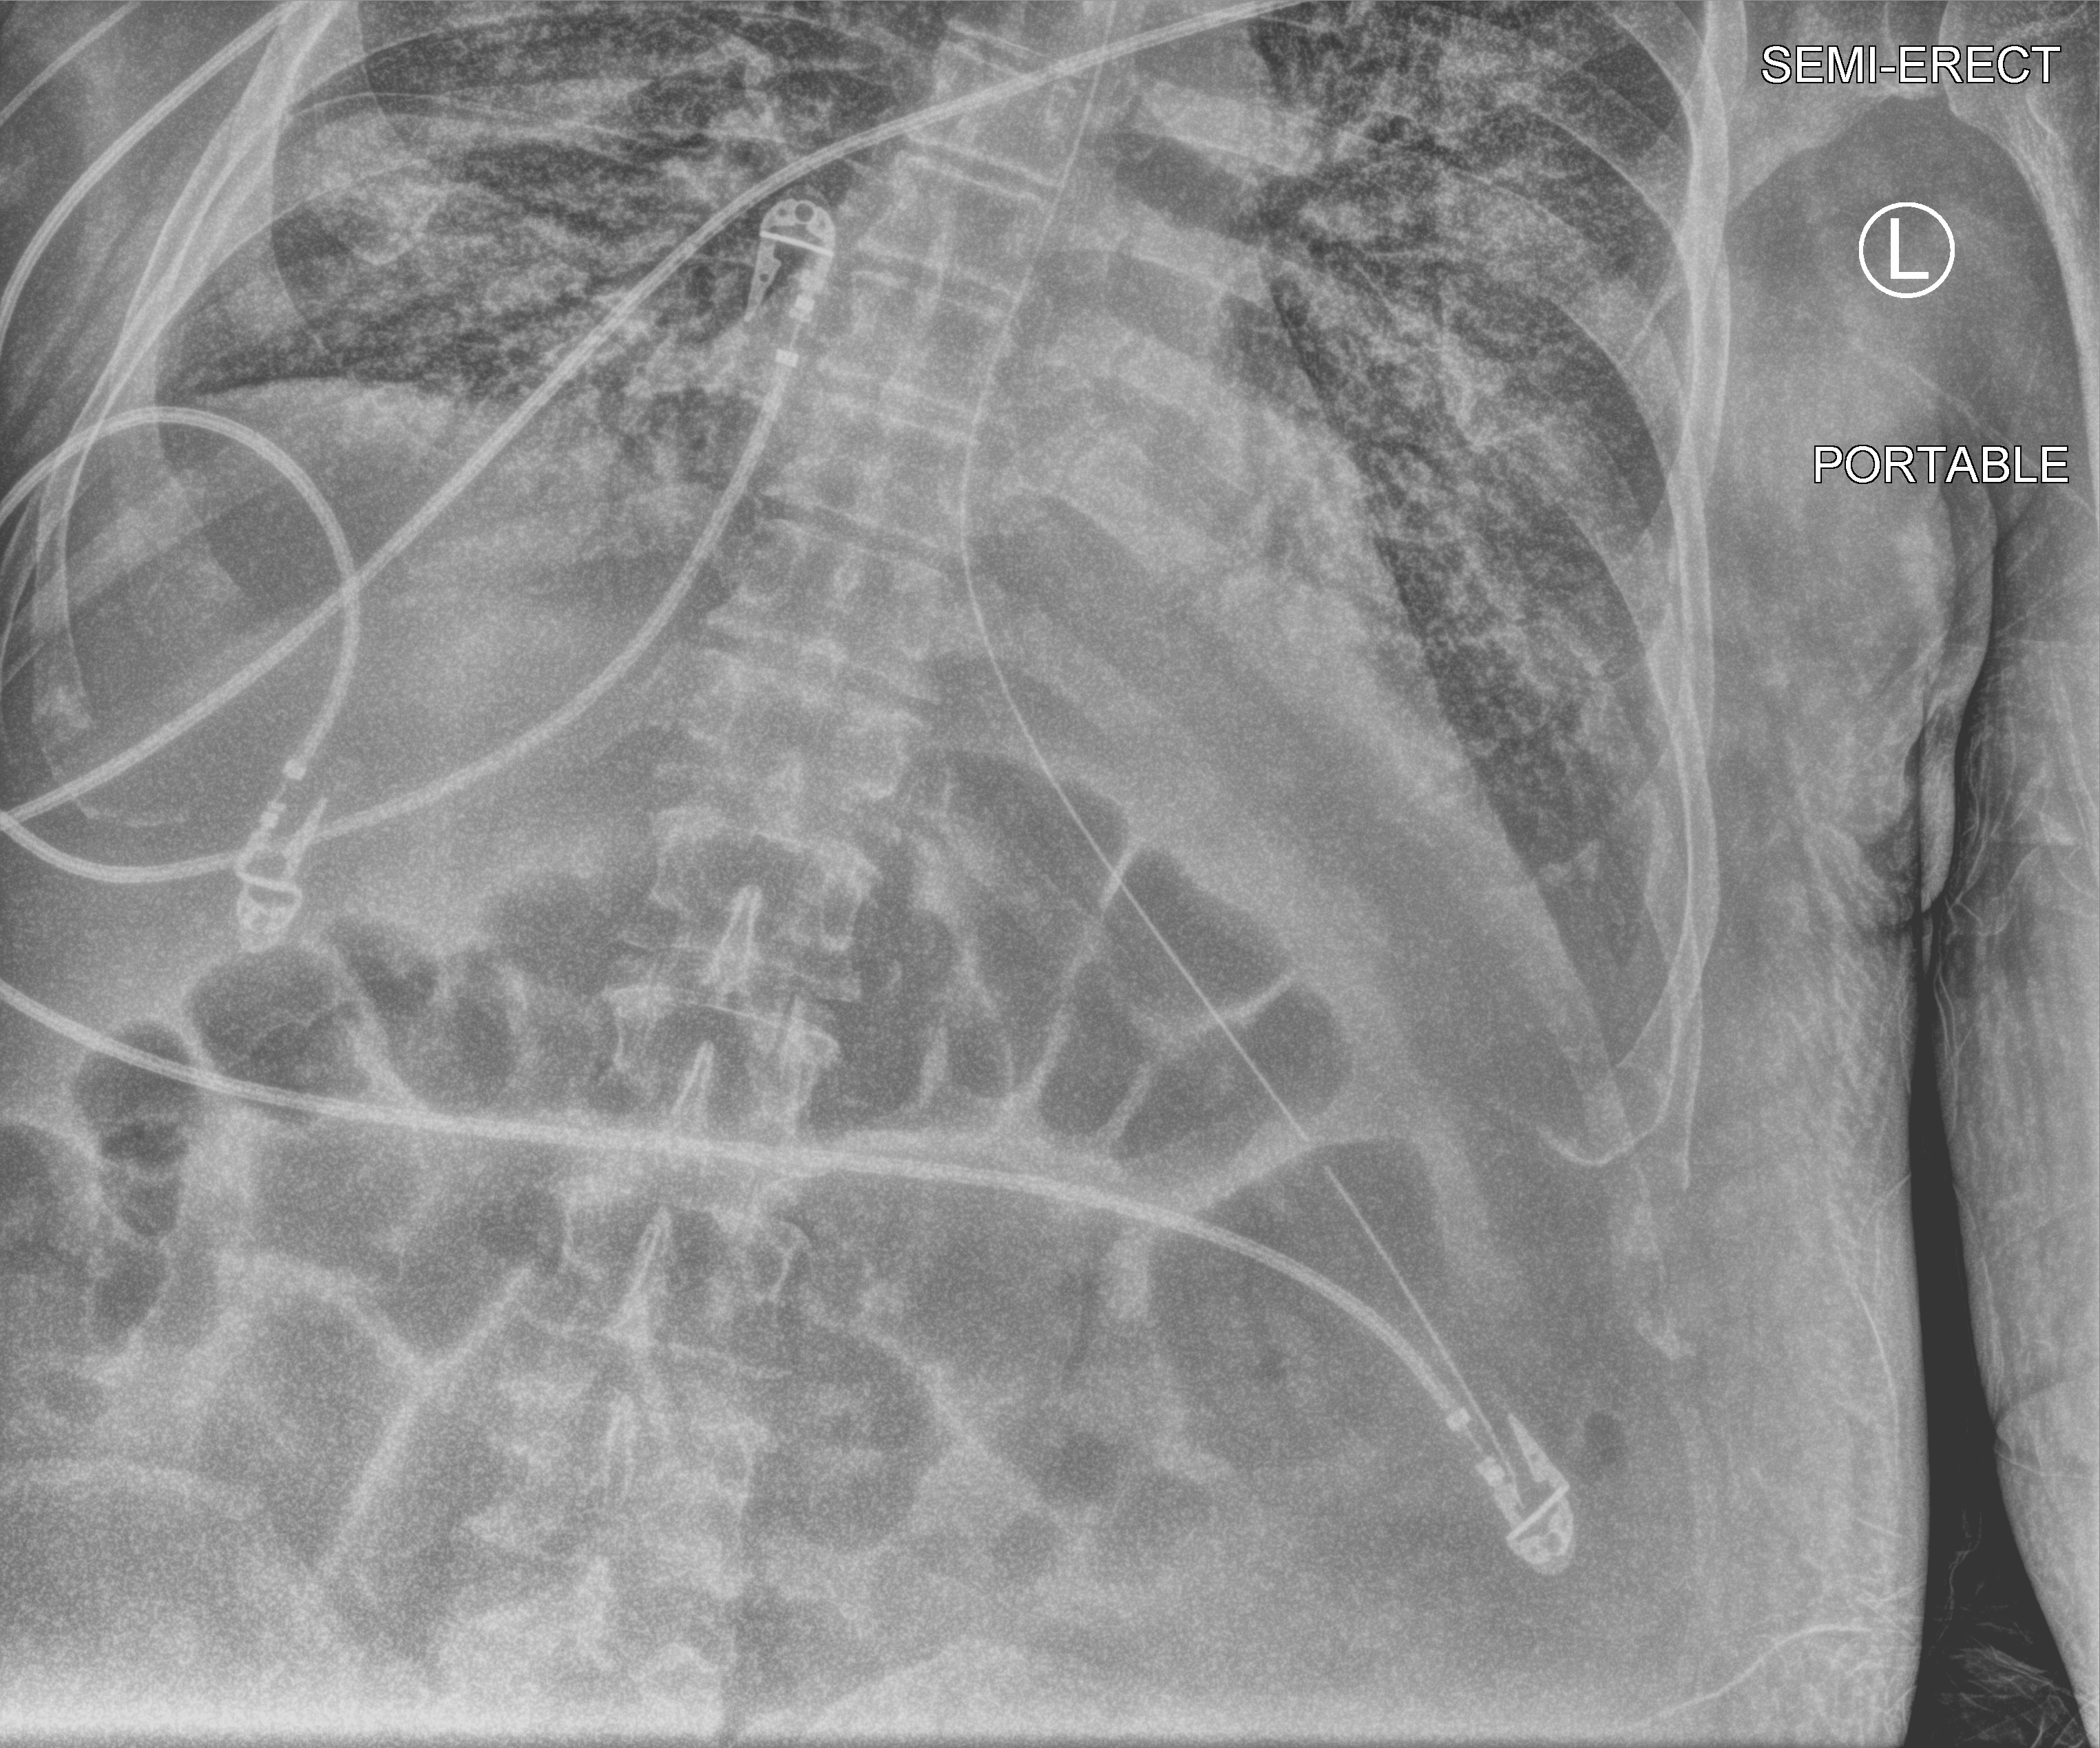
Portable chest radiograph, anteroposterior (AP) projection. Patient hospitalised with COVID-19; male, aged 60–74 years.
From the hospital-stay record, not from the radiograph (when in the stay this image was taken is not recorded): admitted to intensive care during this hospital stay: yes; mechanically ventilated during this hospital stay: yes.